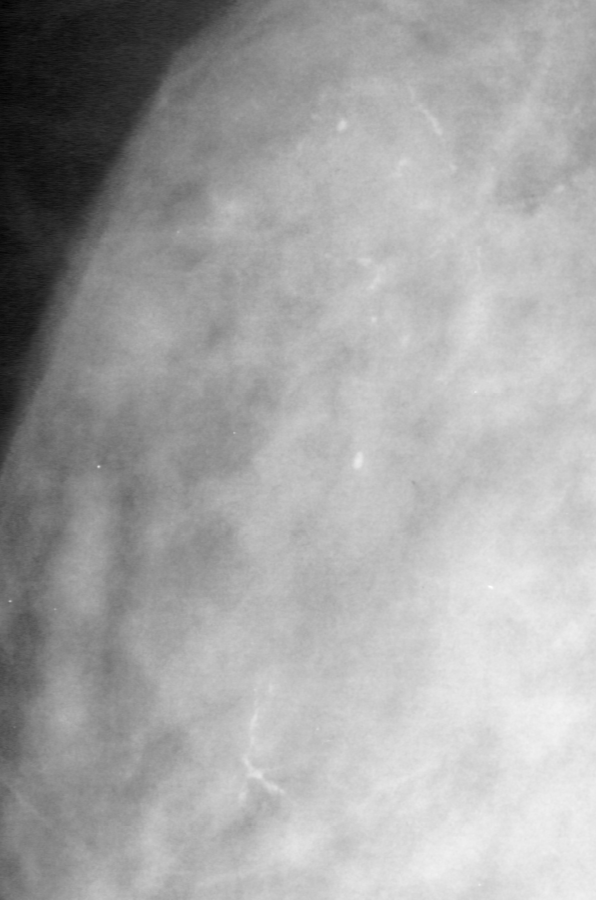
Region of interest cut from a scanned film mammogram (one marked finding), left breast, MLO view, BI-RADS breast density category 4 (scale 1–4).
- Marked abnormality: calcifications, morphology pleomorphic, distribution segmental; BI-RADS assessment category 4; pathology result (as recorded, not read from the image): malignant.